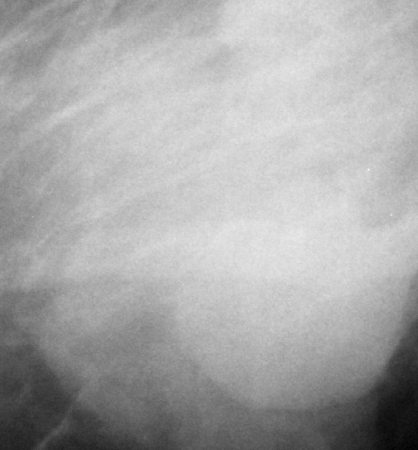
Cropped region of a digitized screen-film mammogram centred on a radiologist-marked abnormality; right breast; MLO view; BI-RADS breast density category 2 (scale 1–4).
Finding: mass, shape lobulated, margins microlobulated; BI-RADS assessment category 5; pathology (as recorded): malignant.